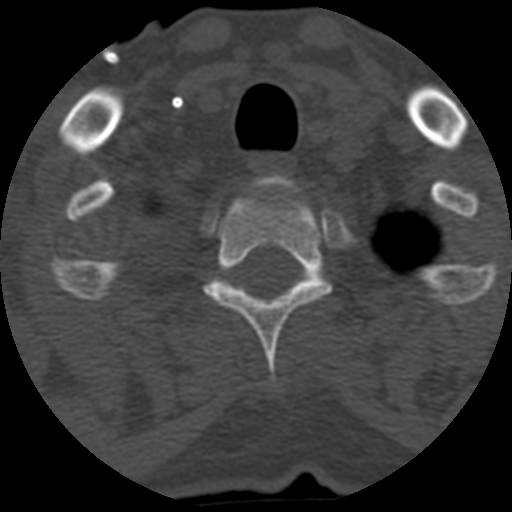
CT including the spine, one axial slice; slice 504 of 708 in the series (ordered by position); reconstruction kernel STANDARD; one of 3 acquisitions stored at this slice position; bone window (W 1800 / L 400 HU); 1.25 mm slice thickness; 512 × 512 image matrix, field of view 160 × 160 mm. Patient age 55 years. From the clinical record (not read from this slice): primary cancer: colon; vertebrae with lytic lesions (as recorded): T12, L1, L5.
Outlined on this slice (semi-automatically segmented with operator editing):
- T1 vertebra: box from (x=259, y=182) to (x=266, y=186) px
- T2 vertebra: (x=203, y=190)–(x=331, y=388)